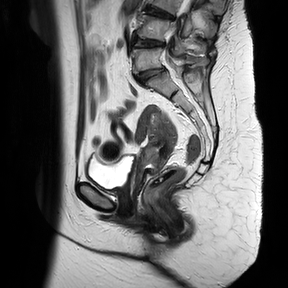
Pelvic MRI for cervical cancer, one sagittal slice; slice 19 of 37 in the series (ordered by position); T2-weighted; 1.5 T; TE 100 ms, TR 4174.1 ms; 288 × 288 image matrix. Female patient, age 65 years.
Annotated regions visible in this slice (expert manual segmentation):
- uterus and cervix: bounding box (x1, y1, x2, y2) in pixels: (136, 111, 178, 189)